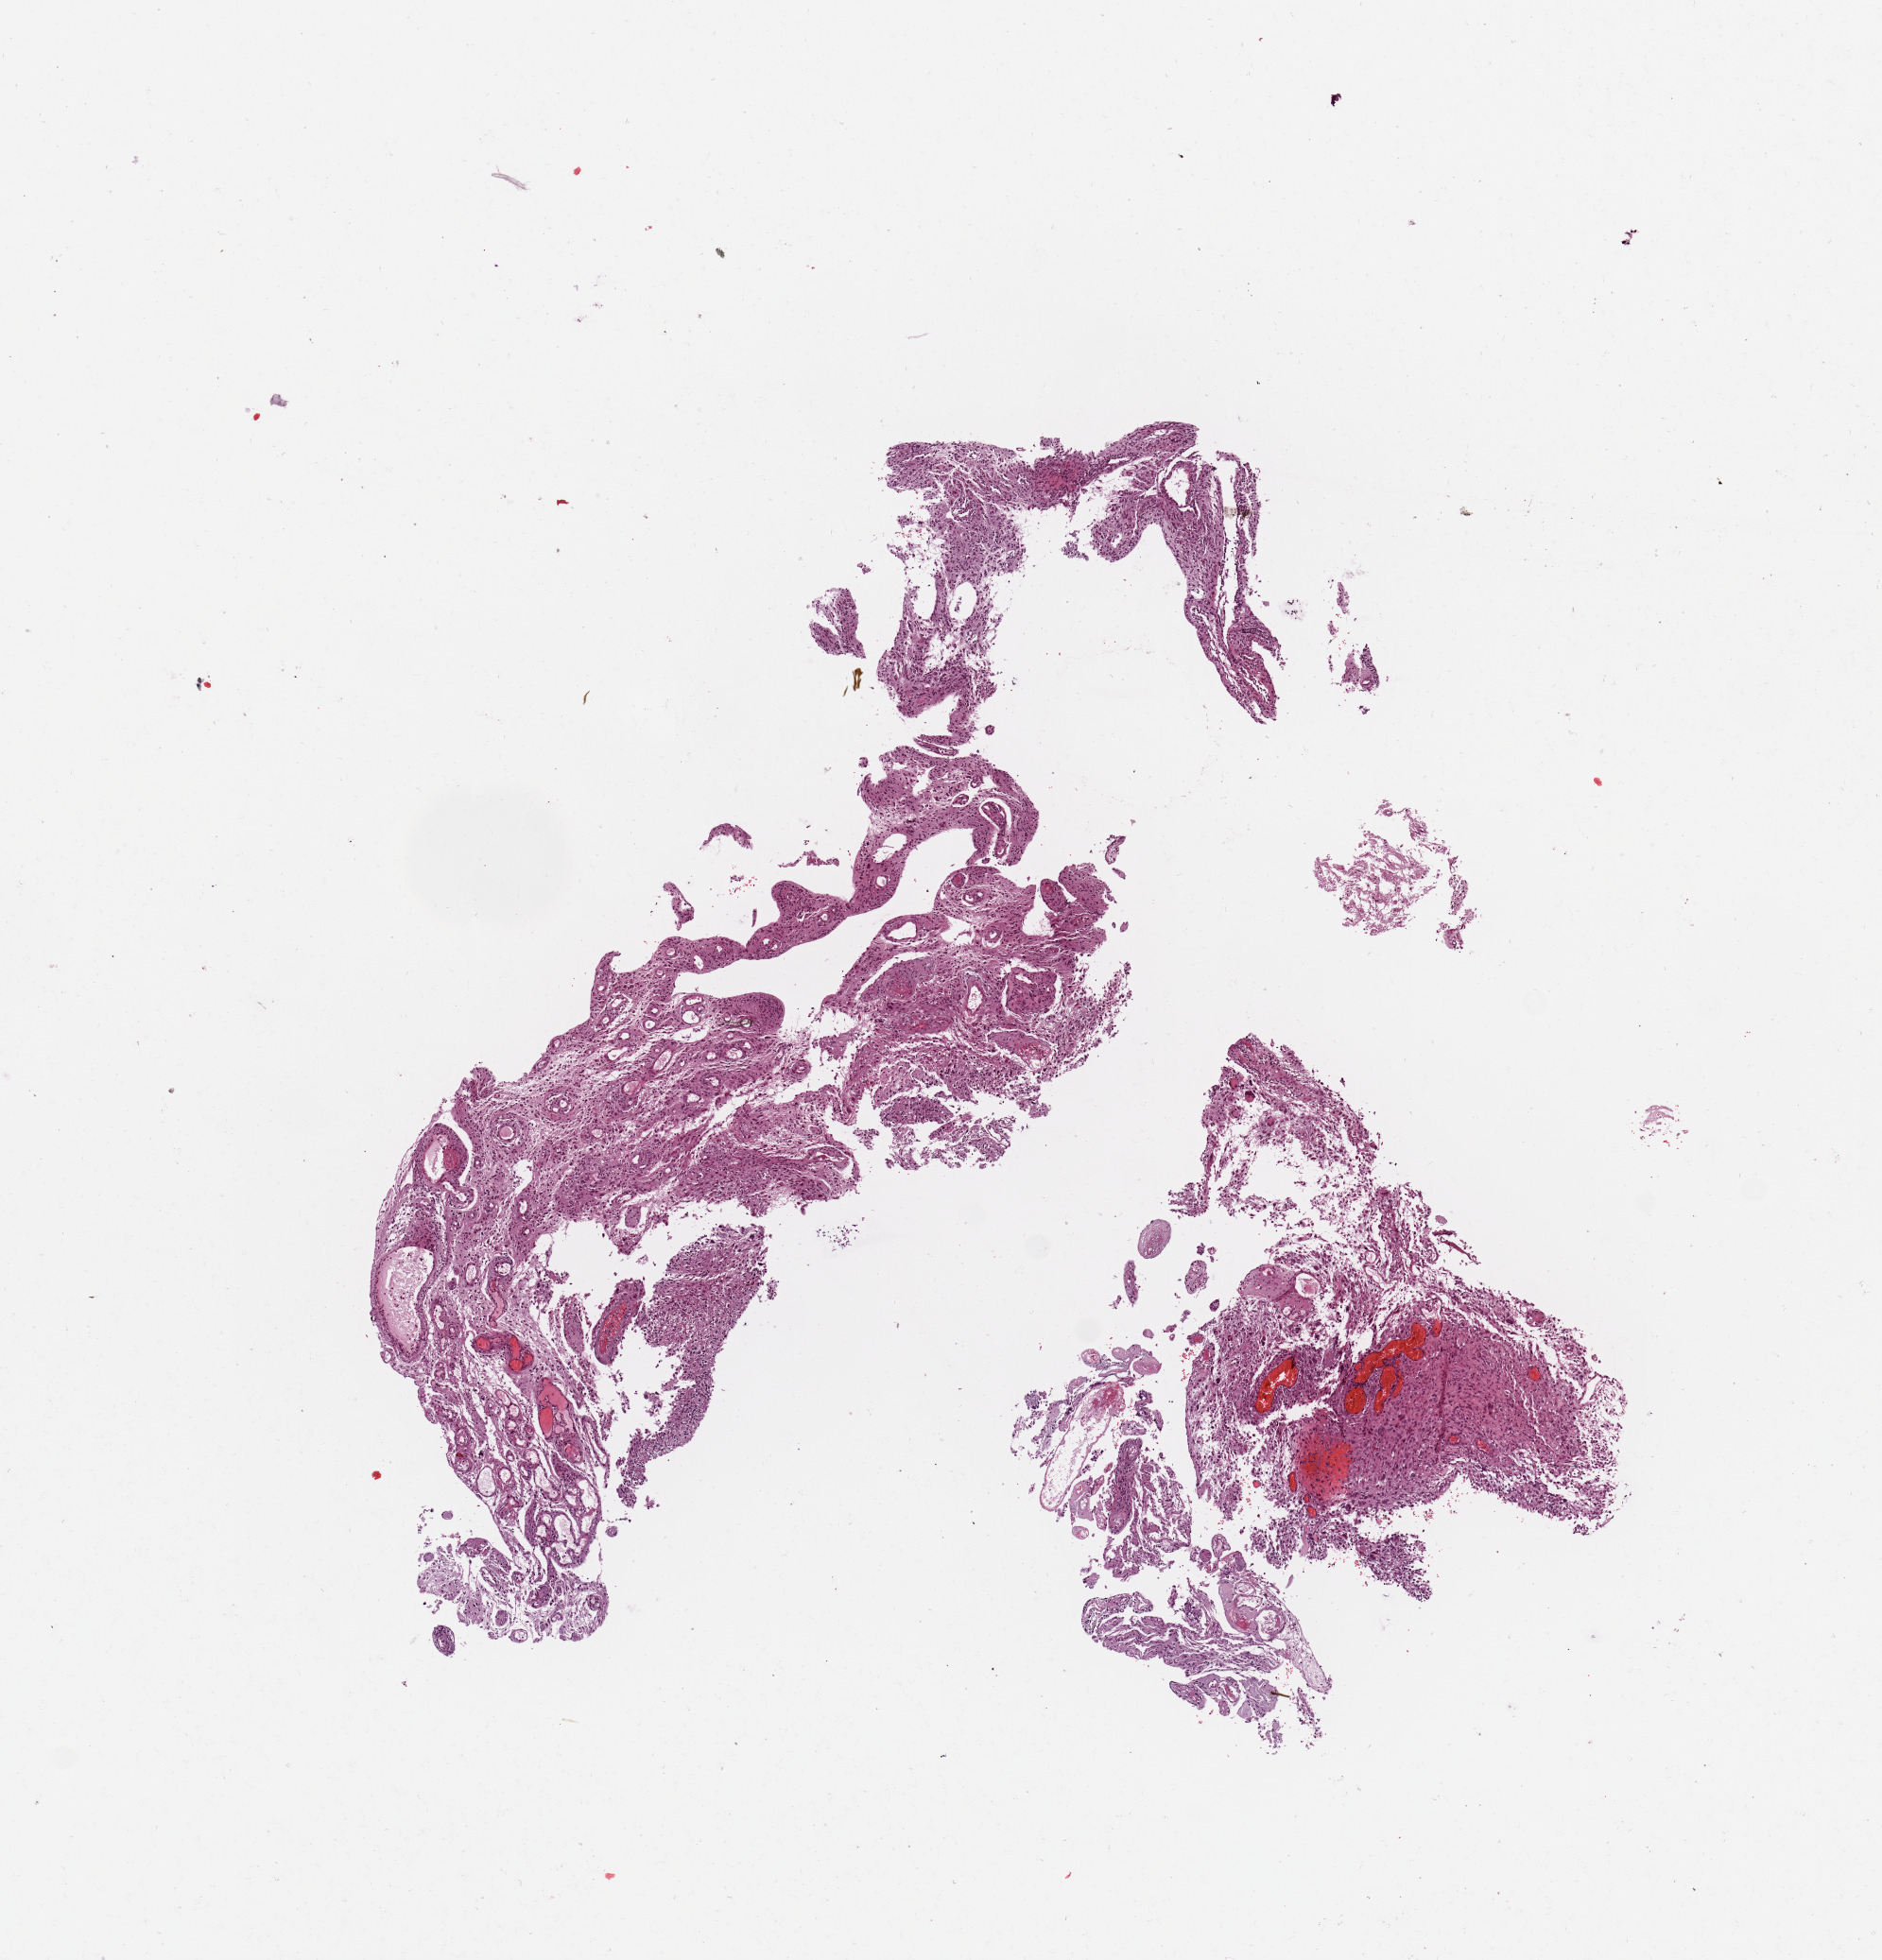
Whole-slide histology image, H&E — low-resolution overview of the scanned area, about 7.9 x 8.2 mm, tumour tissue sample, sampled site: brain. 72-year-old female patient. Composition of this section per pathologist review: tumour nuclei 70%, necrosis 5%.
- histologic diagnosis: Glioblastoma
- primary tumour site (as recorded): temporal lobe